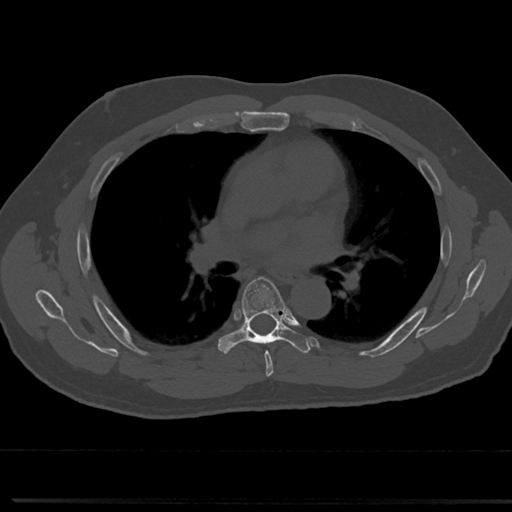
CT including the spine, one axial slice. Slice 462 of 817 in the series (ordered by position). Reconstruction kernel Br40s/3. 120 kVp. Bone window (W 1800 / L 400 HU). 512 × 512 image matrix. Patient: male, 61 years. From the clinical record (not read from this slice): primary cancer: prostate.
Outlined on this slice (semi-automatically segmented with operator editing):
- T5 vertebra: box from (x=247, y=333) to (x=274, y=367) px
- T6 vertebra: (x=217, y=275)–(x=309, y=355)